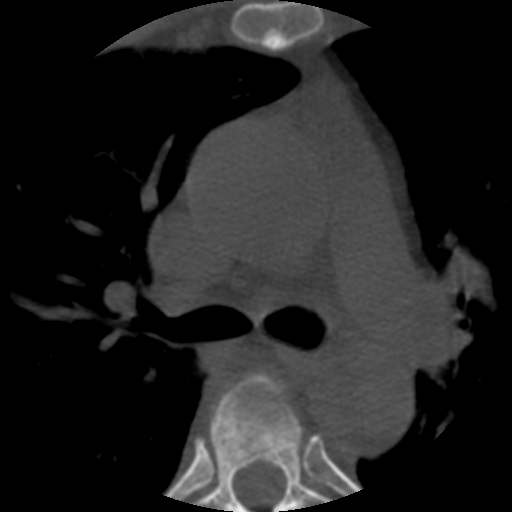
CT including the spine, one axial slice; position 381 of 508 along the scan axis; reconstruction kernel STANDARD; 120 kVp; bone window (W 1800 / L 400 HU); 1.25 mm slice thickness; 512 × 512 image matrix, field of view 160 × 160 mm. Patient age 57 years. From the clinical record (not read from this slice): primary cancer: prostate.
Annotated regions visible in this slice (semi-automatically segmented with operator editing):
- T4 vertebra: bounding box [x1, y1, x2, y2] px = [252, 384, 294, 414]
- T5 vertebra: [195, 373, 329, 512]